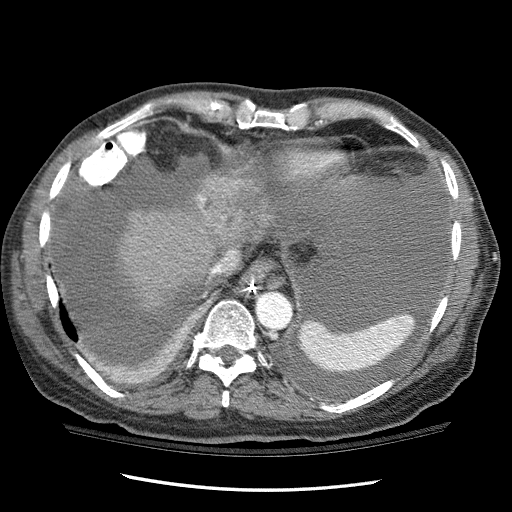
Contrast-enhanced abdominal CT (liver protocol), one axial slice; position 94 of 114 along the scan axis; one of 3 acquisitions stored at this slice position; soft-tissue window (W 400 / L 40 HU); 2.5 mm slice thickness; 512 × 512 image matrix, field of view 360 × 360 mm. From the clinical record (not read from this slice): diagnosis: hepatocellular carcinoma (patient treated with transarterial chemoembolisation; whether this scan precedes or follows treatment is not stated here); TNM stage (as recorded): Stage-I; Child-Pugh class: C.
Annotated regions visible in this slice (semi-automatically segmented with operator editing):
- liver parenchyma outside the tumour (the mass and vessels are separate outlines, so this box may not span the whole liver): bounding box [x1, y1, x2, y2] px = [119, 165, 269, 311]
- mass: [197, 175, 270, 241]